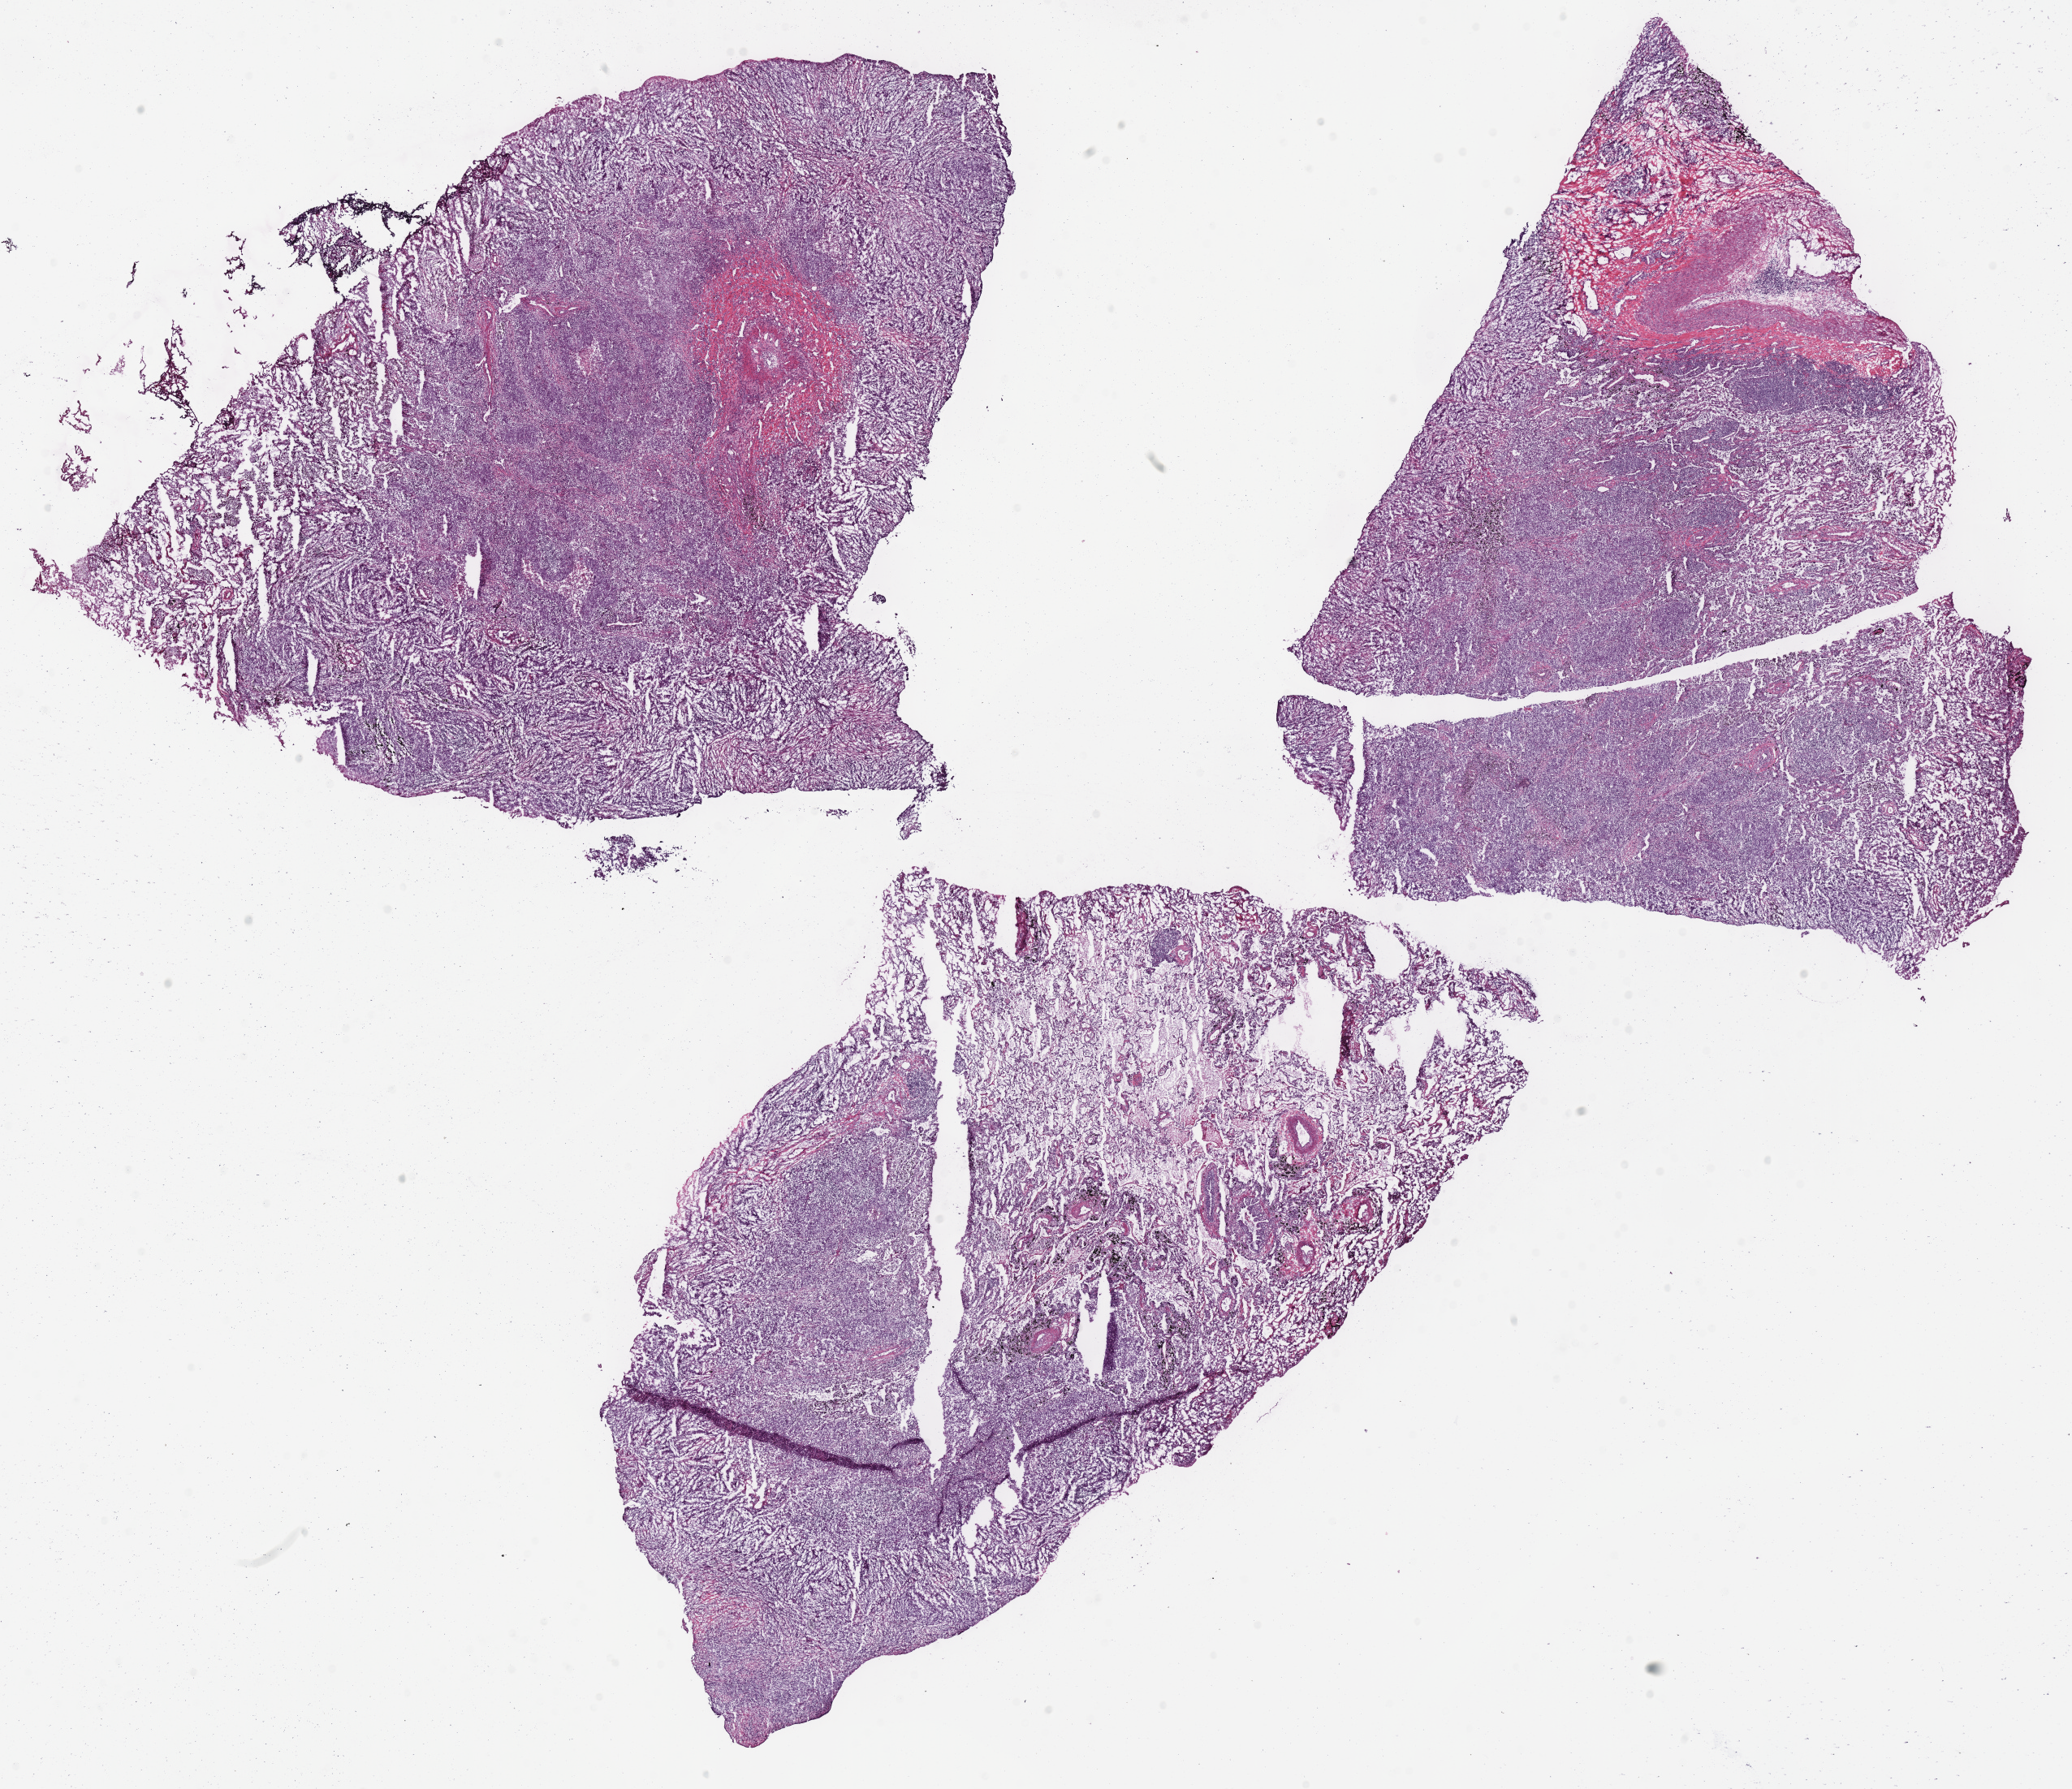
Digitized Hematoxylin and eosin (H&E) stained tissue section (whole slide), whole scanned area (about 20.1 x 17.3 mm) shown as a low-resolution overview, frozen section from the top of the tissue portion, sample: primary tumour, lung. Male, age 62 years at initial diagnosis. Composition of this section per pathologist review: tumour cells 60%, tumour nuclei 65%, normal cells 15%, stromal cells 22%, necrosis 3%. Infiltration values recorded for this section: lymphocyte infiltration 18%, monocyte infiltration 5%, neutrophil infiltration 2%.
AJCC pathologic stage: IA. Pathologic diagnosis: Squamous cell carcinoma, NOS (lower lobe, lung).